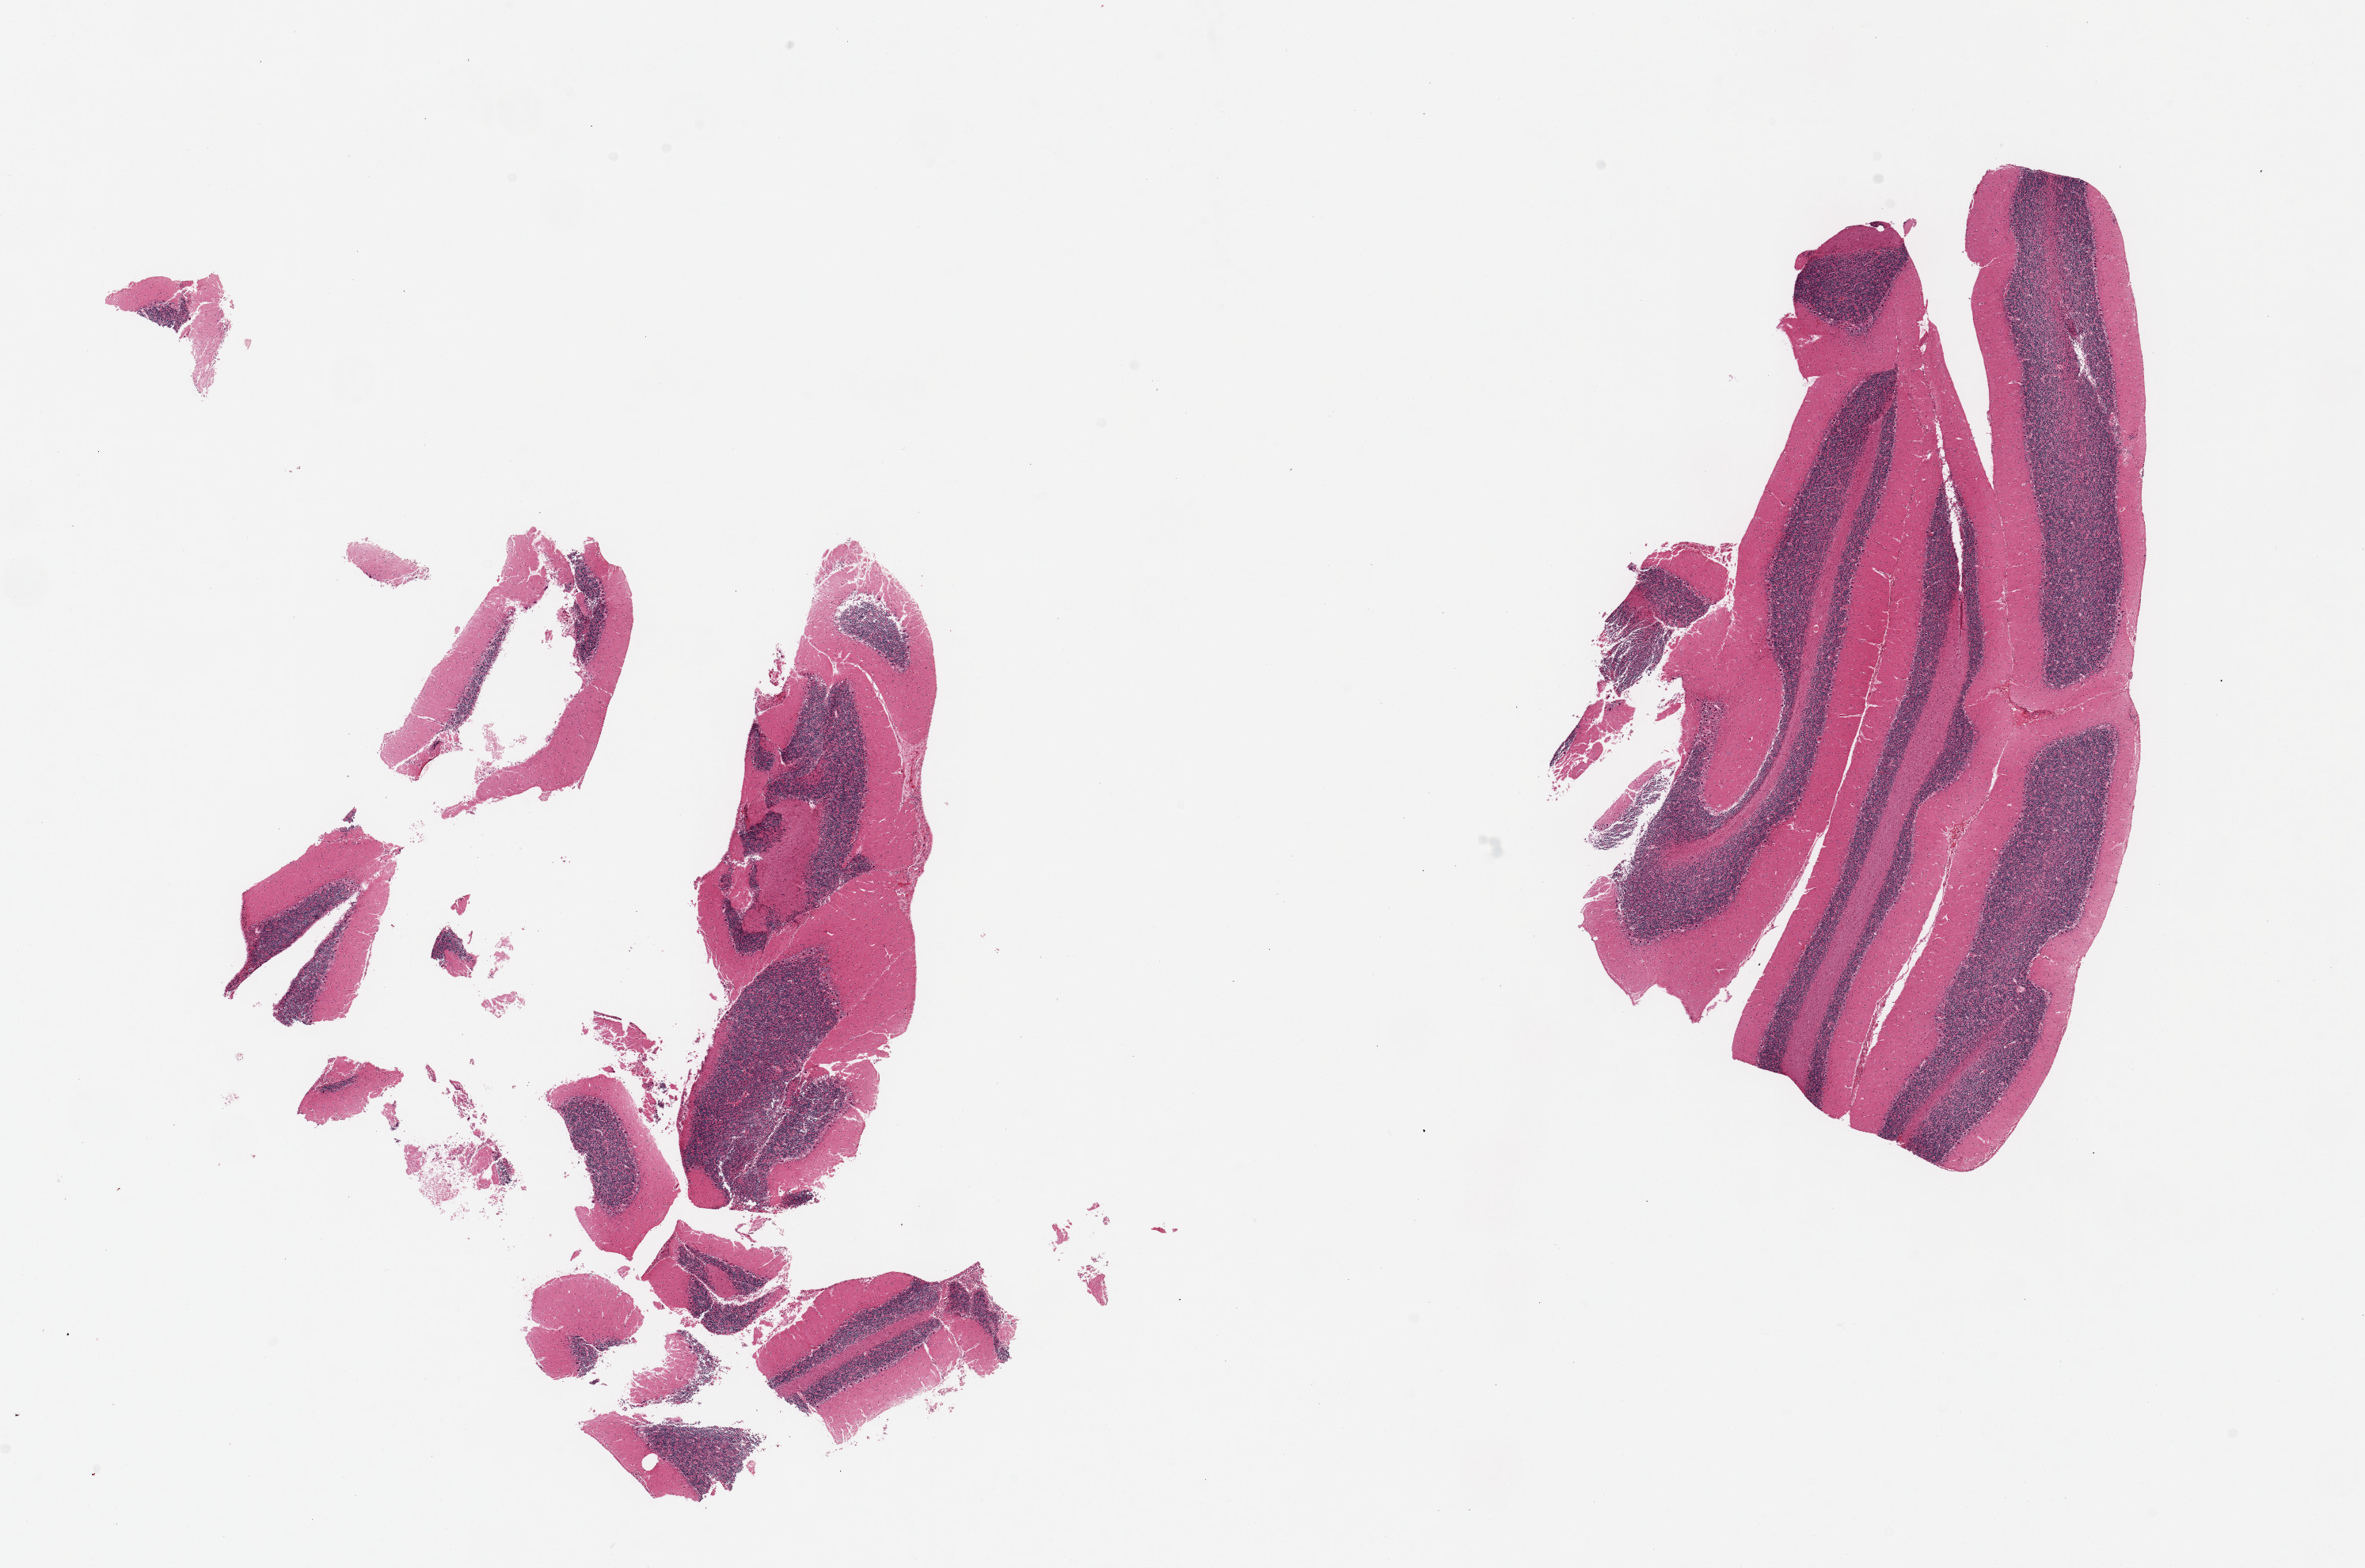
Whole-slide image, H&E stain, brightfield — a low-resolution overview of the entire scanned area, about 23.6 x 15.7 mm (slide scanned at 20x), PAXgene-fixed, paraffin-embedded tissue, section of cerebellum (target tissue), donor tissue sample.
• review note (as recorded): 2 fragmented pieces